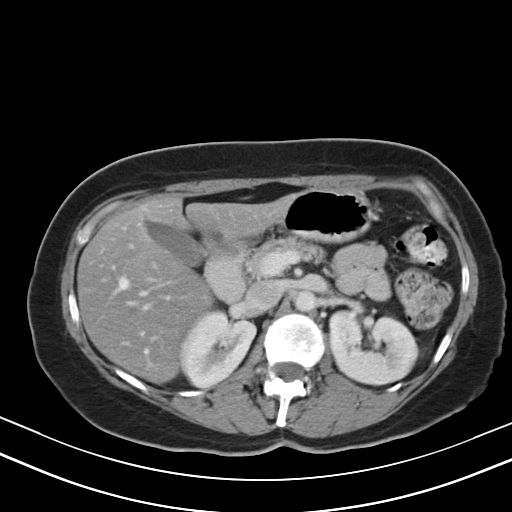
Contrast-enhanced abdominal CT, one axial slice; slice 25 of 47 in the series (ordered by position); reconstruction kernel B40s; 130 kVp; soft-tissue window (W 400 / L 40 HU); 512 × 512 image matrix. Female patient. Case-level facts recorded for this patient, not image findings: diagnosis: colorectal cancer liver metastases, imaged before liver resection; multiple liver metastases: no; largest metastasis: 3.5 cm; disease in both lobes: no.
Outlined on this slice (expert manual segmentation):
- hepatic veins: box from (x=118, y=278) to (x=147, y=352) px
- liver: (x=79, y=196)–(x=286, y=381)
- planned liver remnant (the part of the liver to remain after resection): (x=79, y=196)–(x=287, y=381)
- portal vein (with intrahepatic branches): (x=147, y=278)–(x=155, y=282)